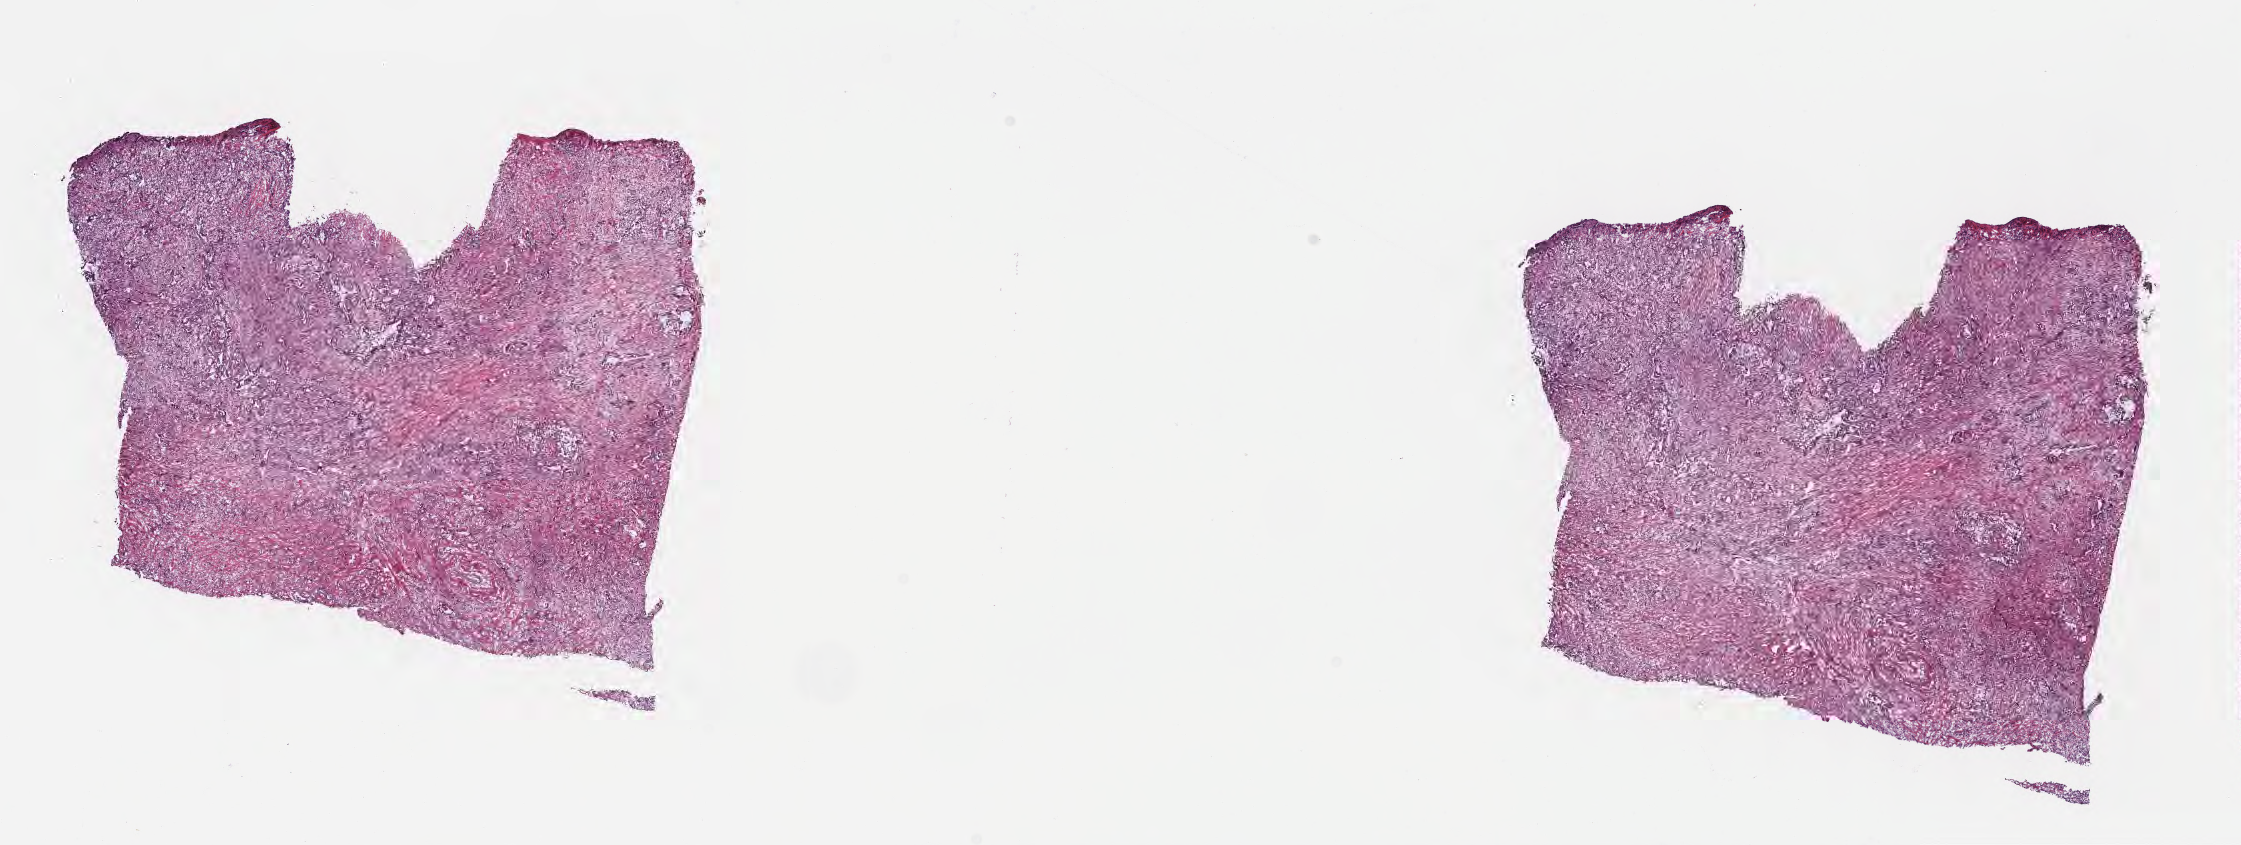
Whole-slide image, H&E stain — a low-resolution overview of the entire scanned area, about 18.1 x 6.8 mm. Cryosection. Primary tumor. Anatomic site: head of pancreas. Female, age 60 years at initial diagnosis. Tumor grade: G3 (poorly differentiated). Slide review estimates, as recorded: tumor cells 31%, tumor nuclei 45%, stromal cells 67%, necrosis 2%, normal cells 0%. Infiltration values recorded for this section: lymphocyte infiltration 46%, monocyte infiltration 4%, neutrophil infiltration 0%.
Histologic diagnosis: Infiltrating duct carcinoma, NOS. Section: bottom of the tissue portion. AJCC pathologic stage: Stage III.